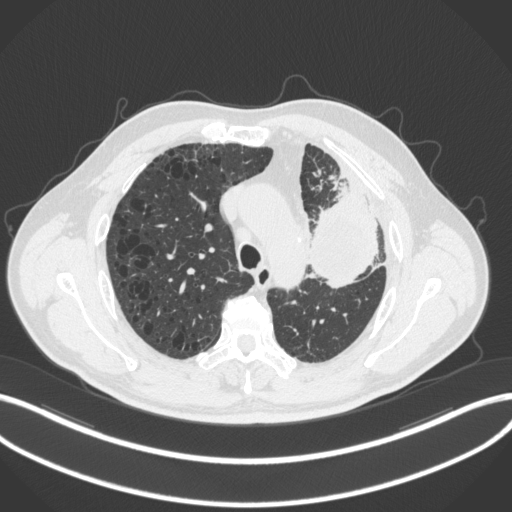
Chest CT, one axial slice; position 216 of 286 along the scan axis; reconstruction kernel B31f; lung window (W 1500 / L -600 HU); 512 × 512 image matrix, field of view 400 × 400 mm. Male patient, age 68 years. From the clinical record (not read from this slice): clinical TNM (as recorded): T3 N3 M1.
Annotated regions visible in this slice (rectangle marked by the reading radiologist):
- lung tumour (recorded histology: adenocarcinoma): bounding box [x1, y1, x2, y2] px = [309, 185, 381, 291]